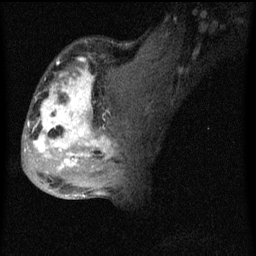
Breast MRI (dynamic contrast-enhanced), one sagittal slice; dynamic contrast-enhanced series, image 2 of 4 at this slice position (ordered by acquisition); 1.5 T; TE 4.2 ms, TR 8 ms; 256 × 256 image matrix, field of view 180 × 180 mm. Patient: female, 50 years.
Outlined on this slice (semi-automatically segmented with operator editing):
- analysis volume of interest (the breast-tissue region the enhancement analysis was run in; not a lesion): bounding box [x1, y1, x2, y2] px = [26, 44, 124, 177]
- tumour enhancement mask (voxels above the 70 % enhancement threshold inside the analysis volume of interest): [26, 58, 115, 167]